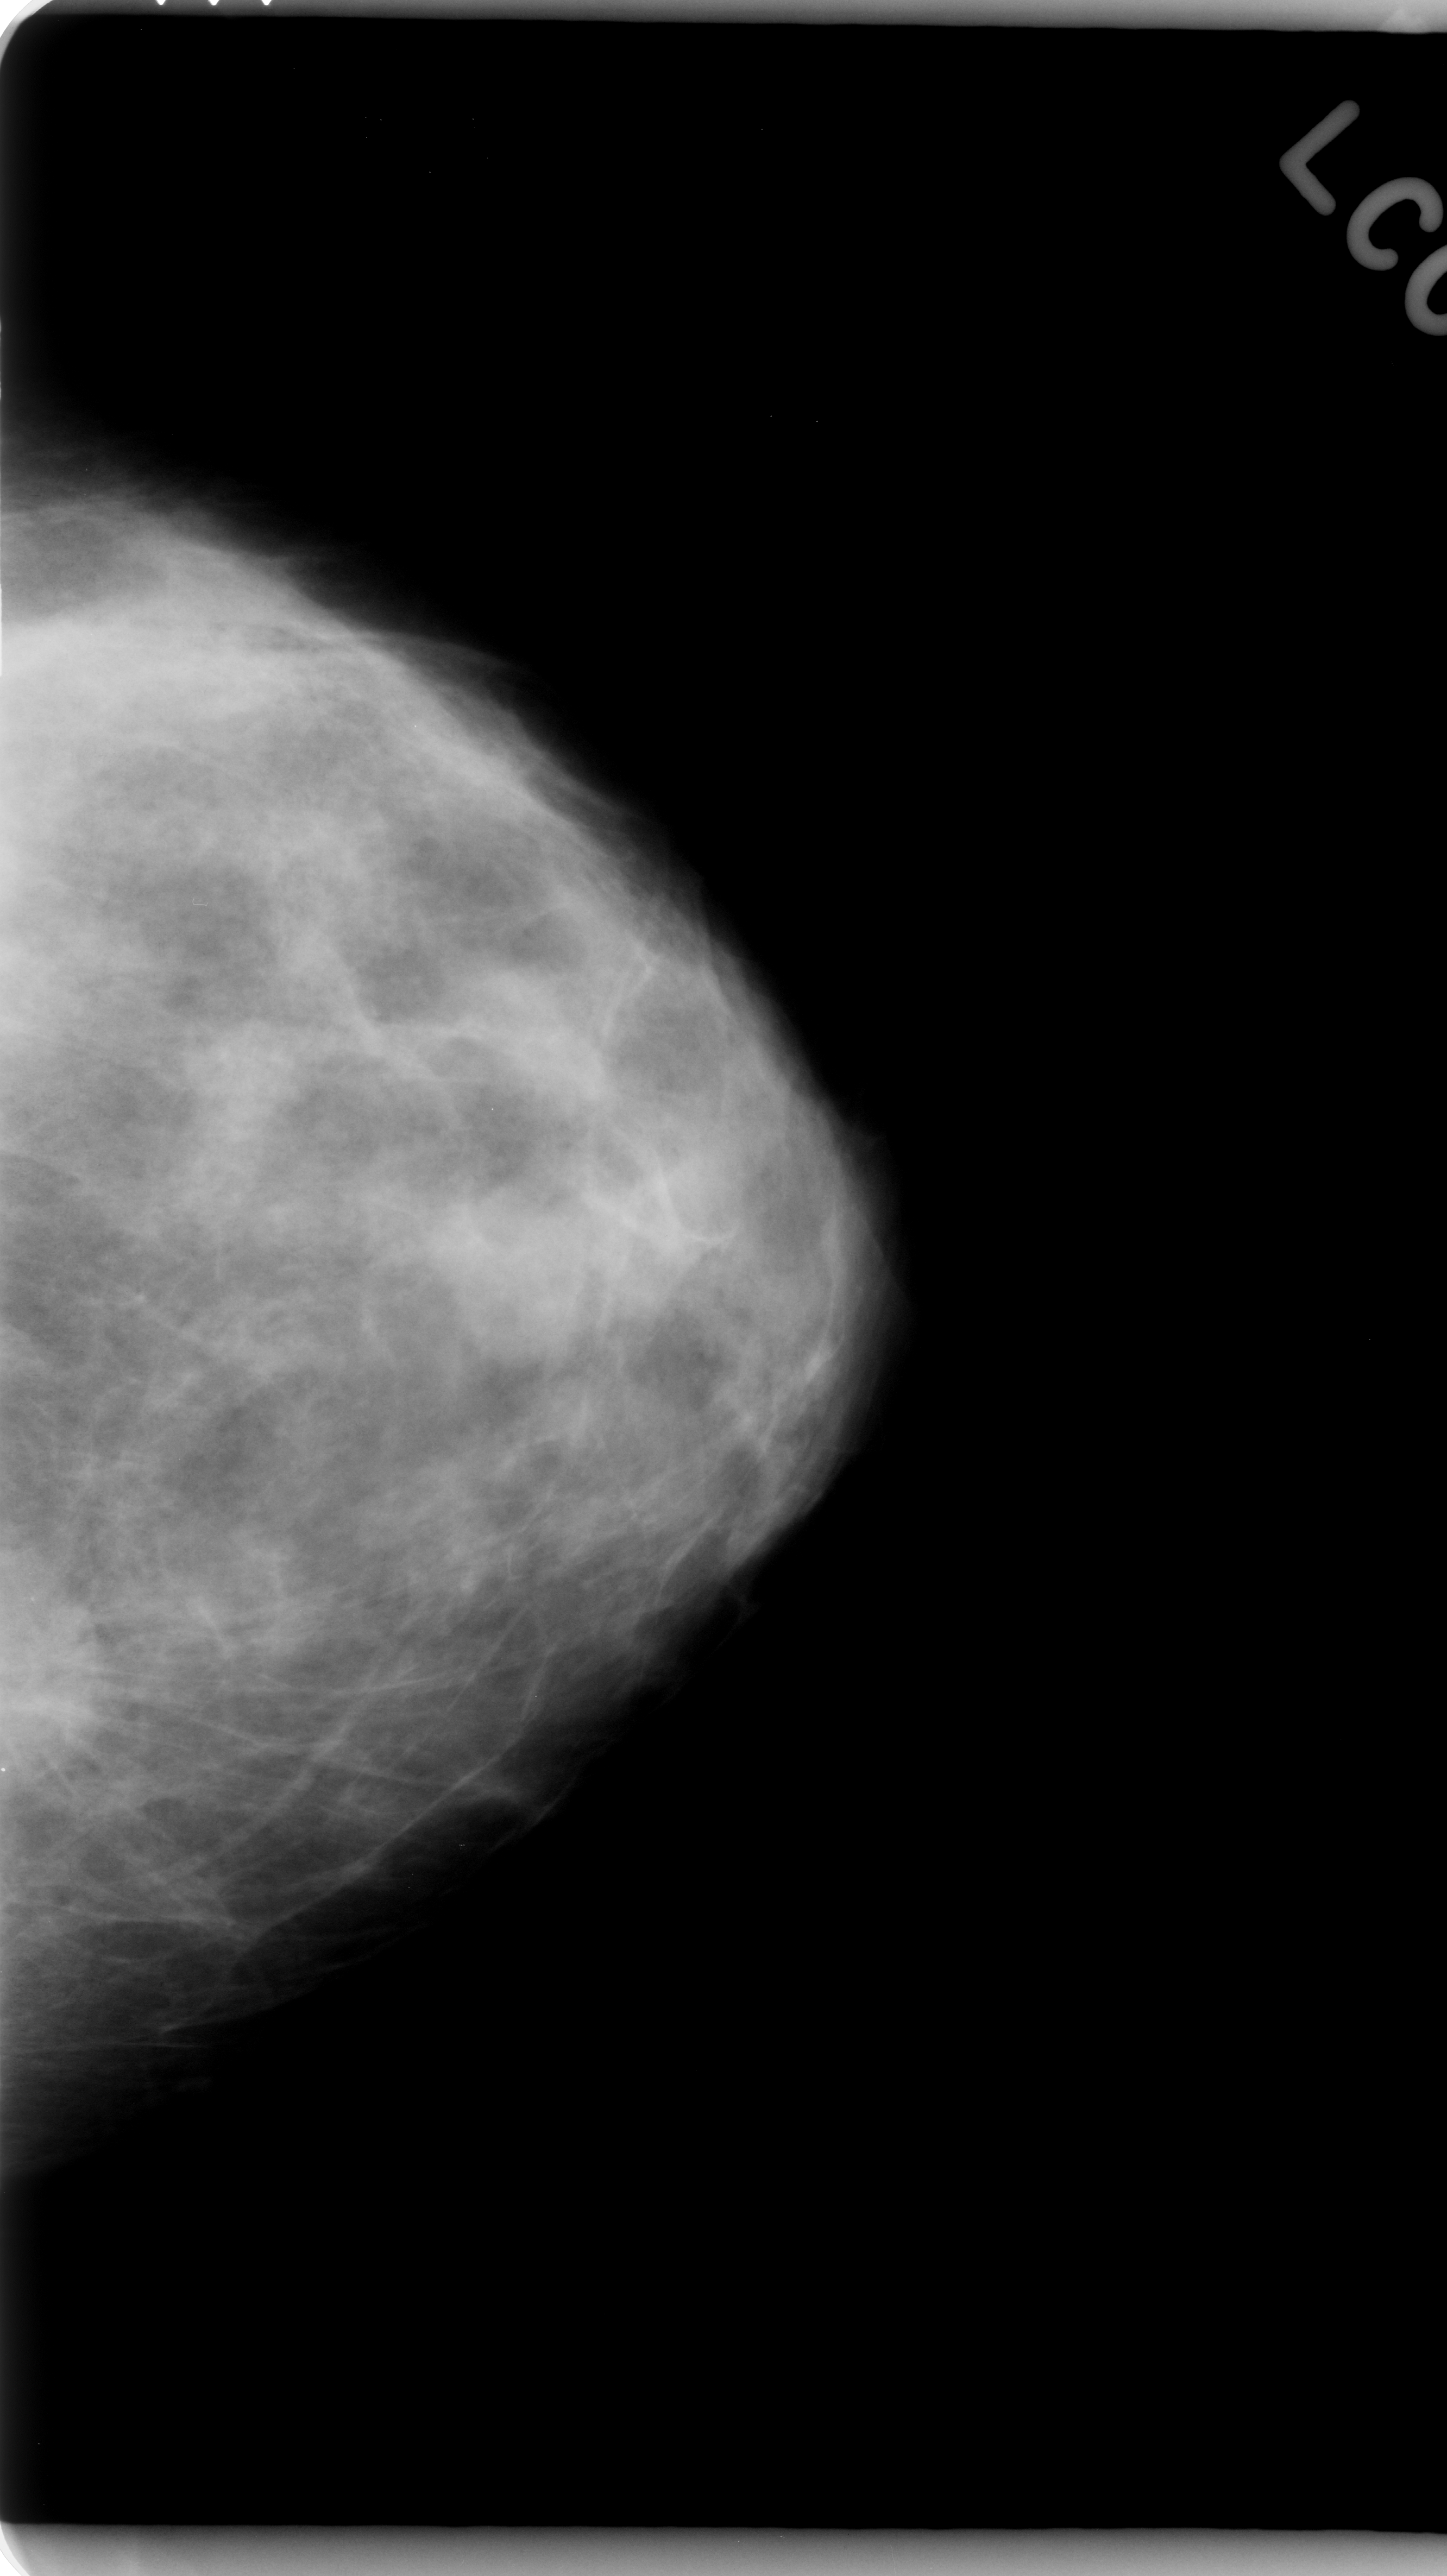
Mammogram (digitized film); left breast; craniocaudal (CC) view; BI-RADS breast density category 3 (scale 1–4).
- Marked findings (only marked abnormalities are described; nothing is implied about the rest of the image): mass, shape irregular, margins spiculated; BI-RADS assessment category 5; subtlety rating 5 on a 1 (subtle) to 5 (obvious) scale; pathology (as recorded): malignant.